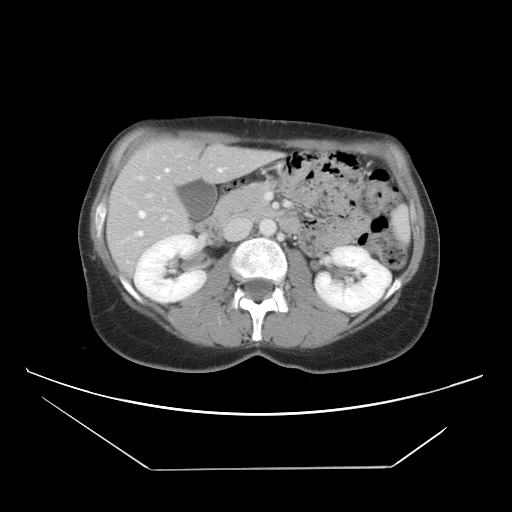
Contrast-enhanced abdominal CT, one axial slice. Slice 21 of 42 in the series (ordered by position). 120 kVp. Intravenous contrast given. Soft-tissue window (W 400 / L 40 HU). 512 × 512 image matrix, field of view 399 × 399 mm. Female patient, age 52 years. From the clinical record (not read from this slice): diagnosis: colorectal cancer liver metastases, imaged before liver resection; multiple liver metastases: yes; largest metastasis: 5.5 cm; disease in both lobes: yes.
Annotated regions visible in this slice (outlined manually by an expert reader):
- hepatic veins: bounding box <128,154,225,238> (left, top, right, bottom; pixels)
- liver: <108,139,273,271>
- planned liver remnant (the part of the liver to remain after resection): <115,139,216,208>
- portal vein (with intrahepatic branches): <148,164,270,221>